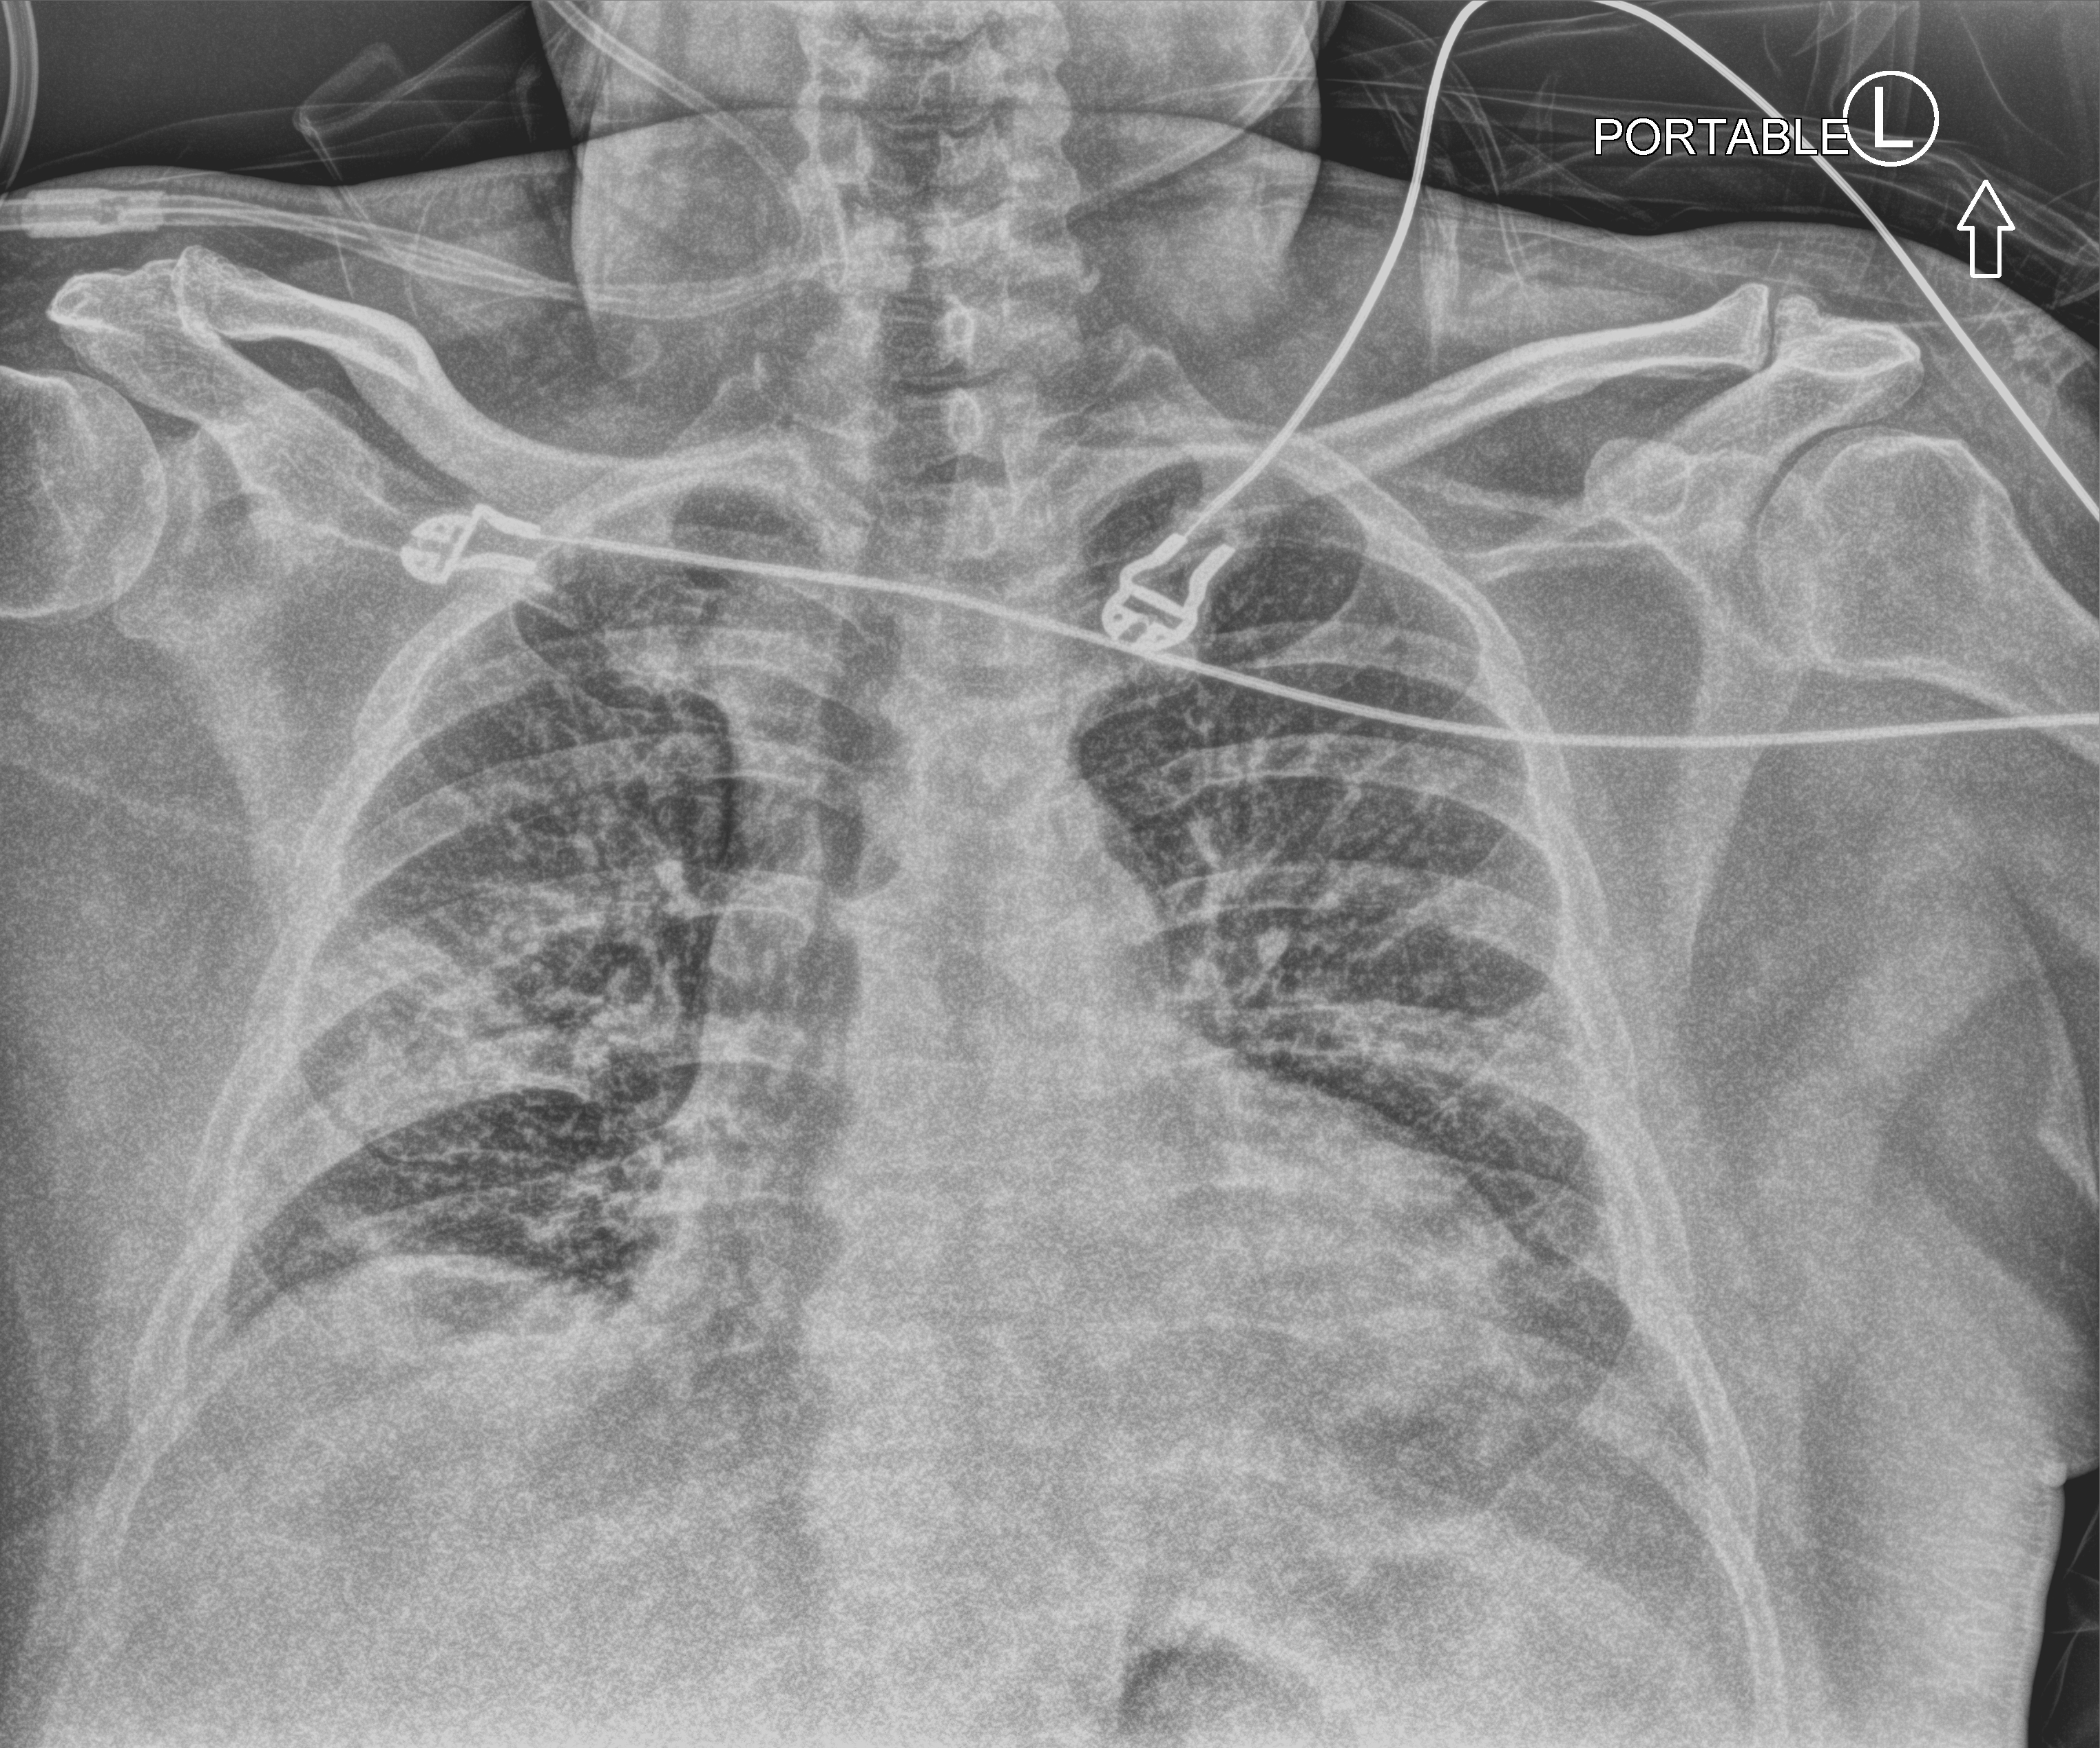
Bedside chest radiograph (computed radiography), anteroposterior (AP) projection. Patient hospitalised with COVID-19; male, aged 18–59 years.
Hospital-stay facts (about this admission, not read from this image; timing relative to this image not recorded): mechanically ventilated during this hospital stay: yes.